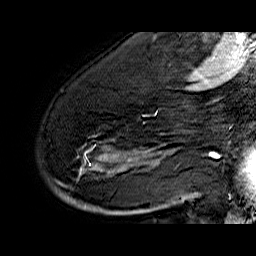
Breast MRI (dynamic contrast-enhanced), one sagittal slice; dynamic contrast-enhanced series, time point 2 of 6 at this slice position (early post-contrast); 1.5 T; TE 6.4 ms, TR 32.9 ms; 4 mm slice thickness; 256 × 256 image matrix. Female patient. Case-level facts recorded for this patient, not image findings: setting: breast cancer imaged before/during neoadjuvant chemotherapy; receptor status: HR-positive, HER2-negative.
Annotated regions visible in this slice (semi-automatic segmentation, software-assisted and operator-edited):
- analysis volume of interest (the breast-tissue region the enhancement analysis was run in; not a lesion): bounding box (x1, y1, x2, y2) in pixels: (55, 74, 176, 210)
- tumour enhancement mask (voxels above the 100 % enhancement threshold inside the analysis volume of interest): (70, 112, 173, 201)